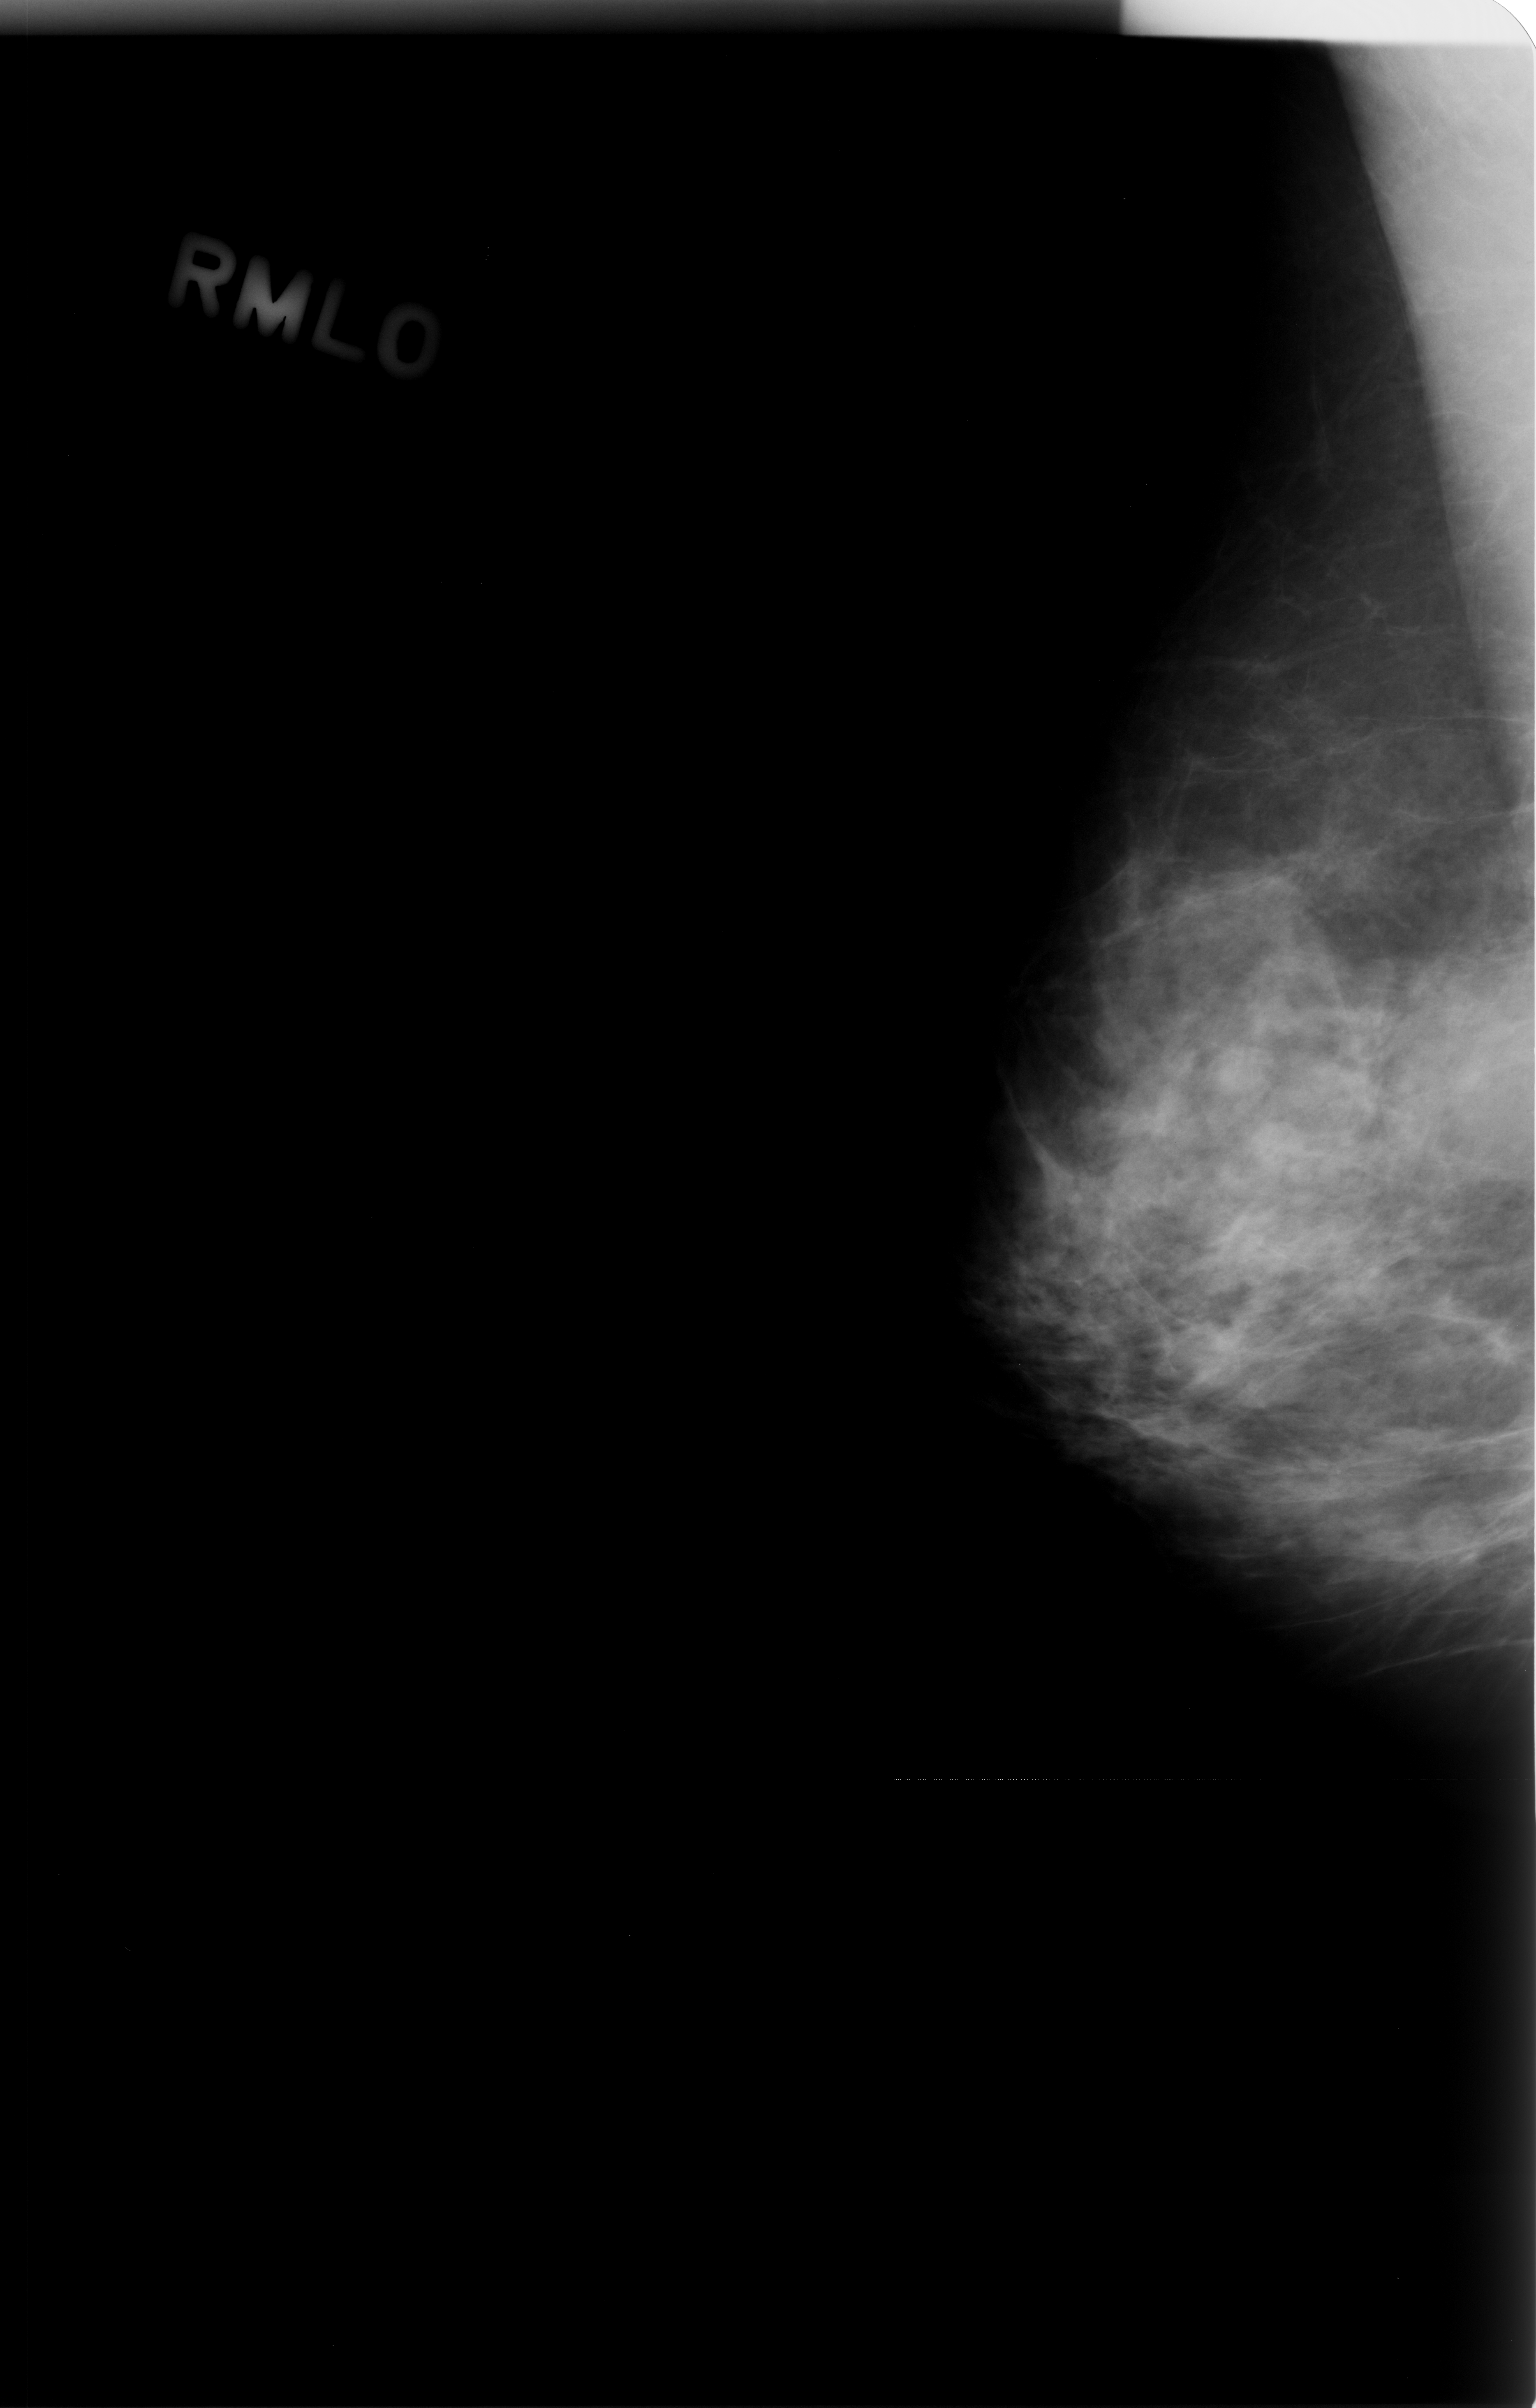
Scanned film-screen mammogram, right breast, mediolateral oblique (MLO) view.
Marked abnormality: mass, shape oval, margins obscured; BI-RADS assessment category 3; subtlety rating 4 on a 1 (subtle) to 5 (obvious) scale; pathology (as recorded): benign.